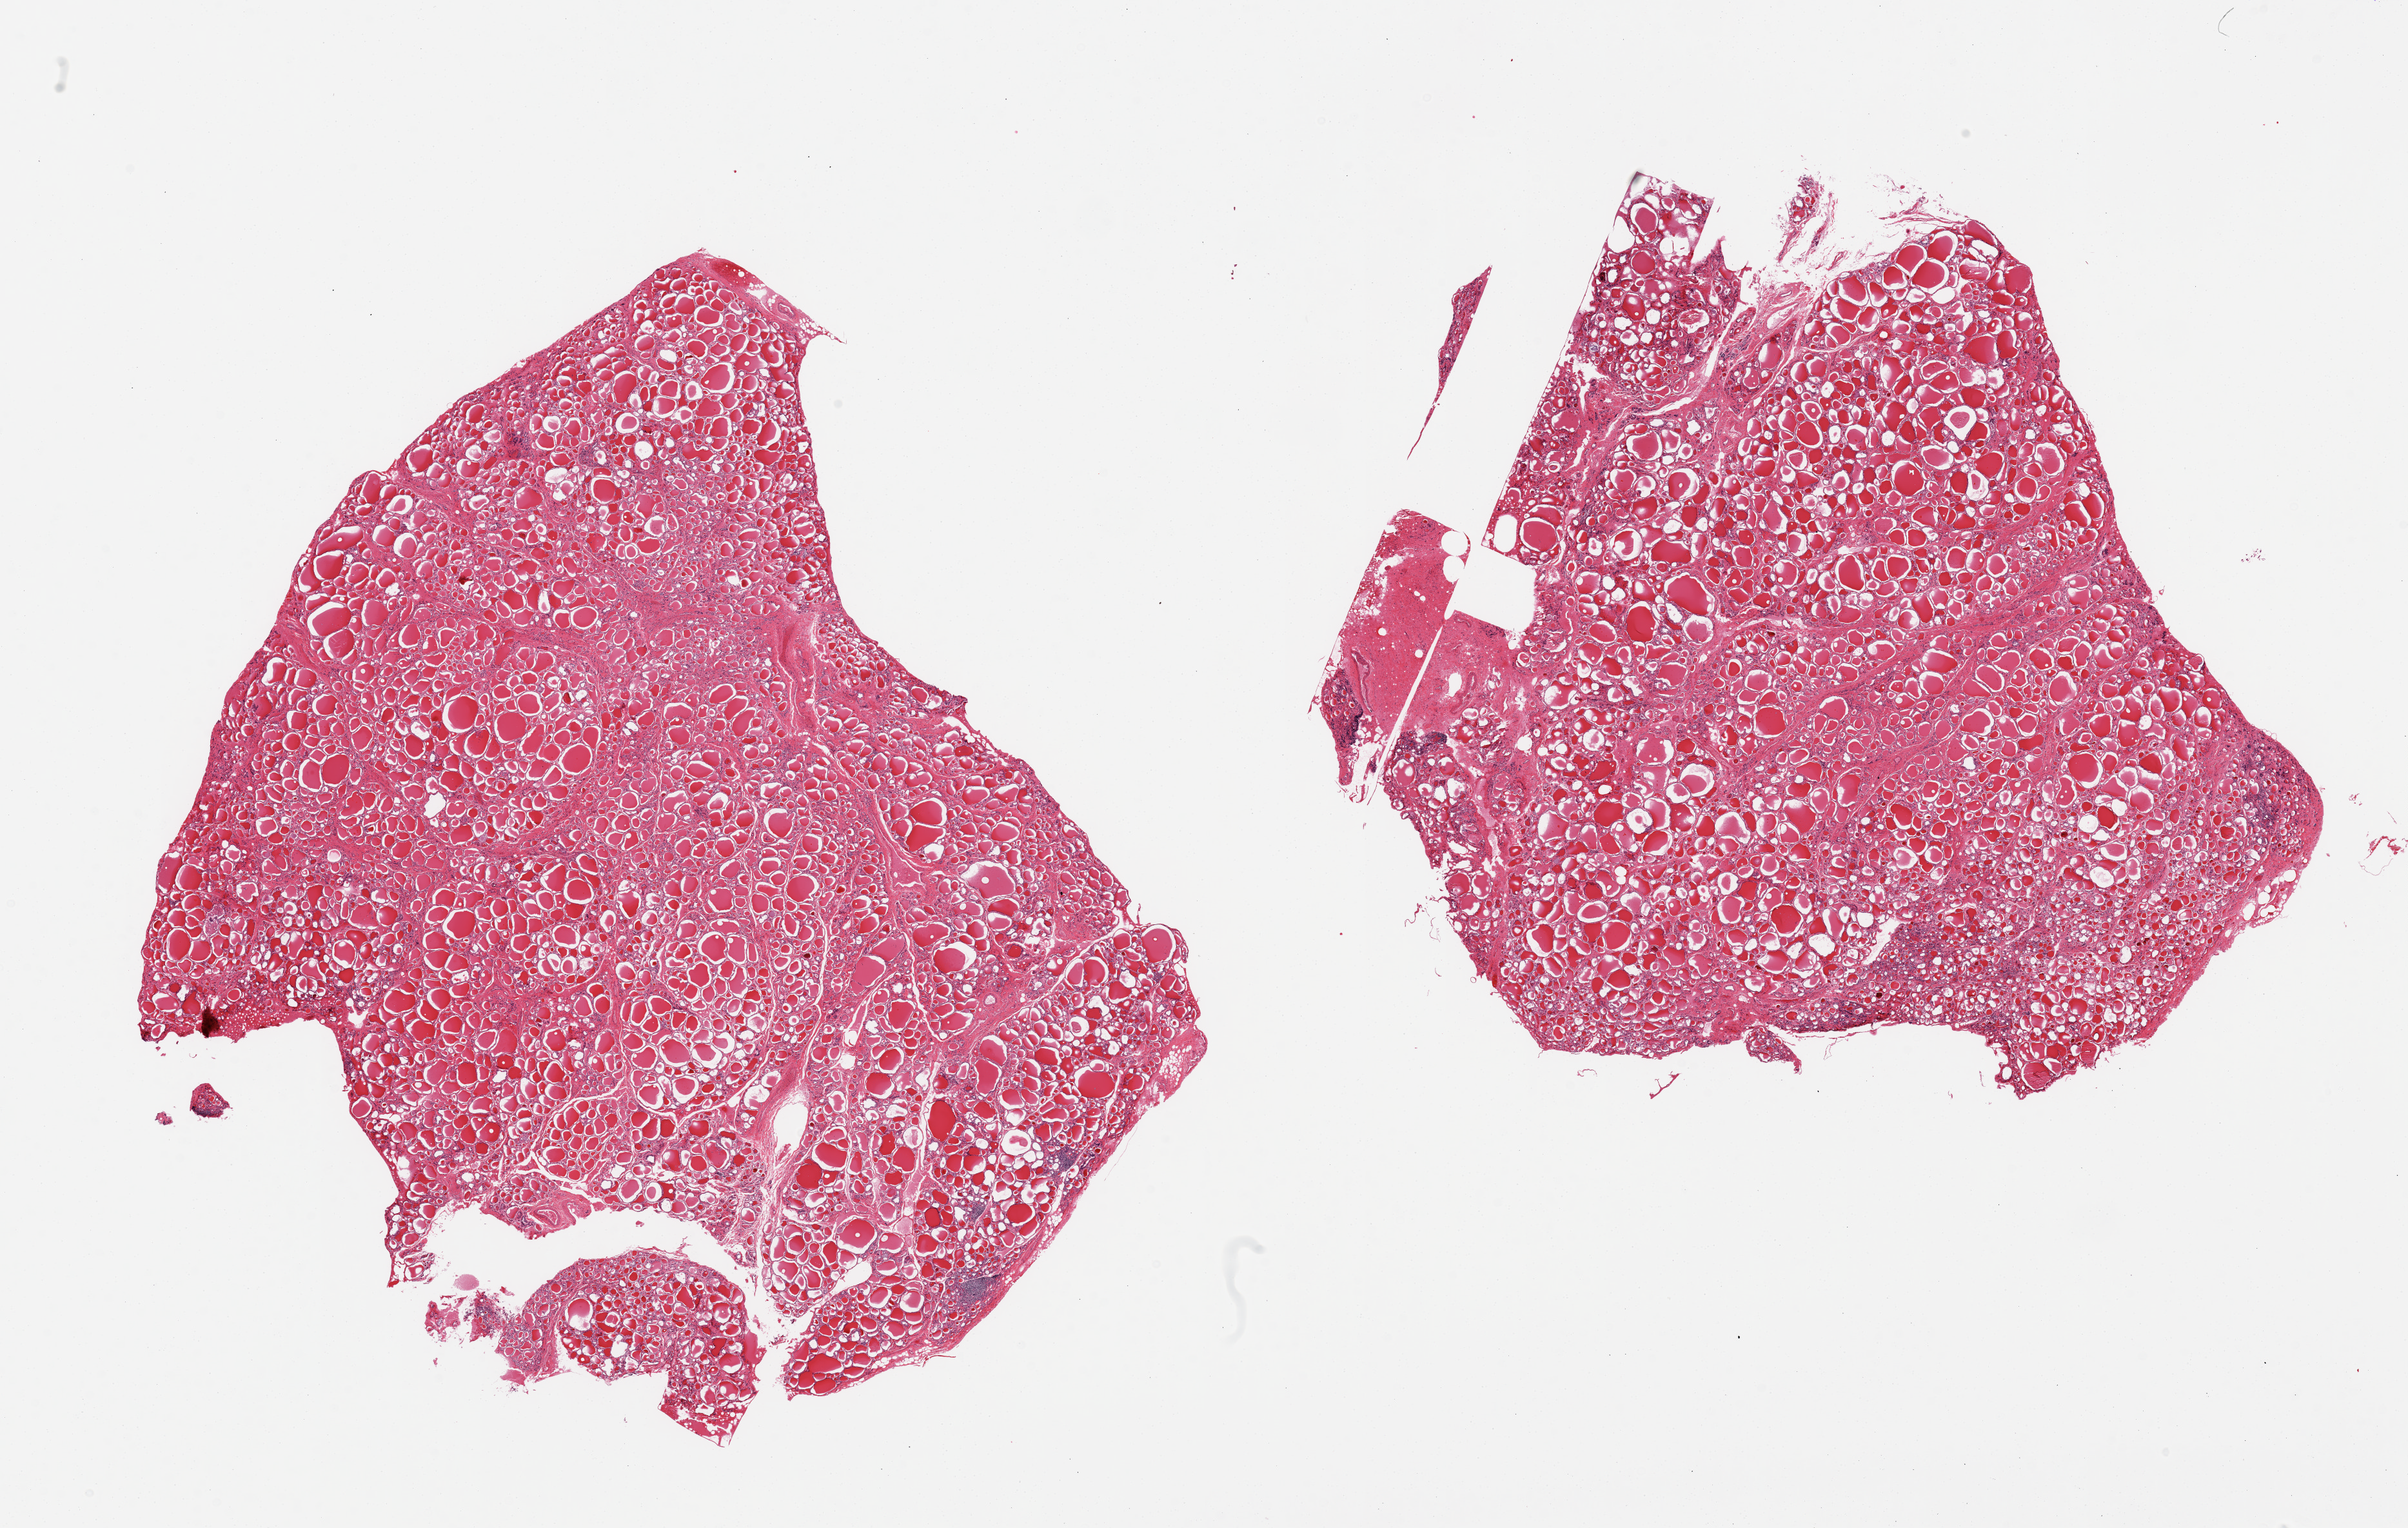
Digitized haematoxylin and eosin-stained section, brightfield, low-resolution overview of the scanned area, about 29.5 x 18.7 mm; PAXgene-fixed, paraffin-embedded tissue; sampled site (target tissue): thyroid; donor tissue sample.
Reviewer comment on this tissue sample: 2 pieces, some fibrosis and nodularity, few collections of lymphocytes.